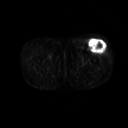
FDG PET of an extremity soft-tissue mass (from a PET/CT study), one axial slice. Position 230 of 267 along the scan axis. 128 × 128 image matrix, field of view 500 × 500 mm. Patient: male, 64 years. From the clinical record (not read from this slice): histological type: extraskeletal osteosarcoma; grade: high; site of the primary tumour: thigh.
Outlined on this slice (expert contour drawn on MRI and transferred to this co-registered scan by the dataset authors):
- gross tumour volume (mass): bounding box <89,40,107,53> (left, top, right, bottom; pixels)